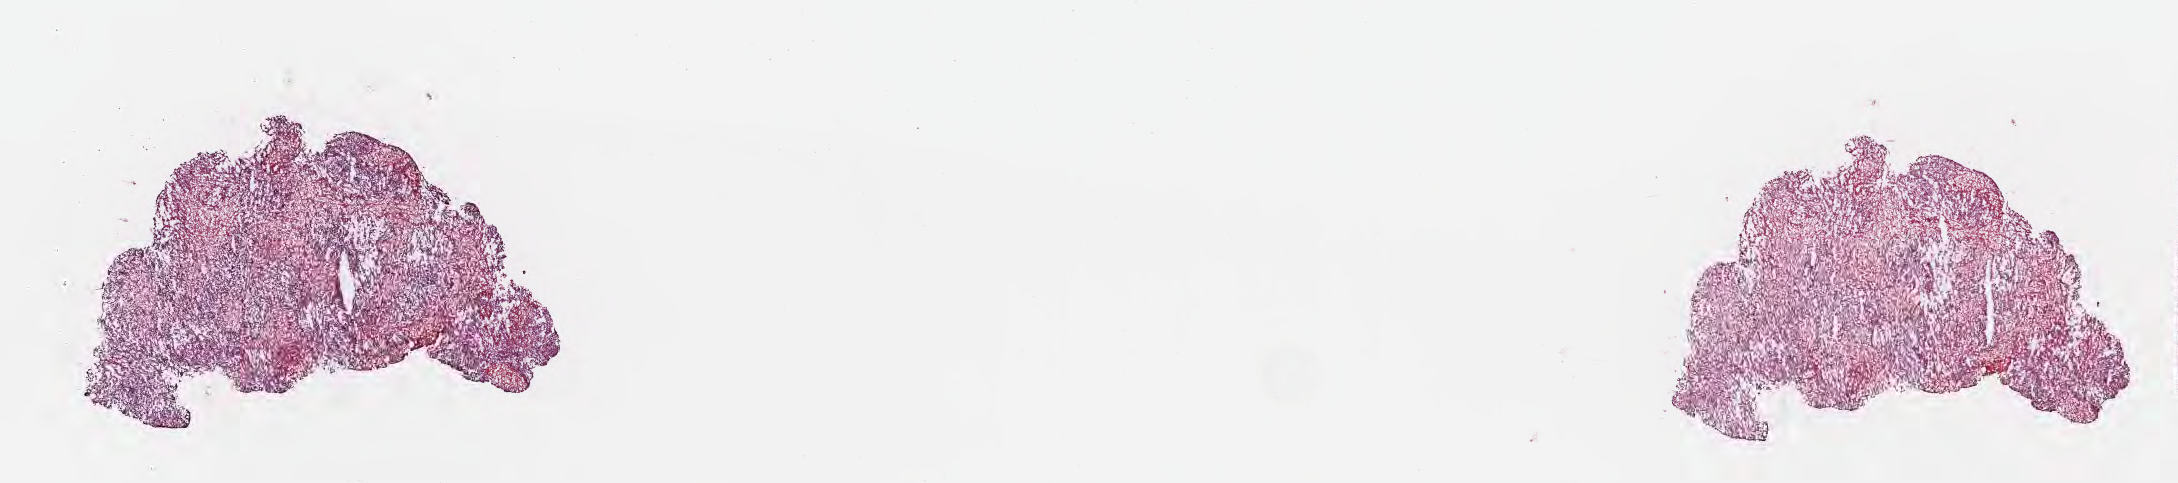
Whole-slide image, haematoxylin and eosin stain — whole scanned area (about 17.6 x 3.9 mm) shown as a low-resolution overview, frozen section (tissue freezing medium), specimen: metastatic tumor tissue, resected from brain. Patient: male, age at initial diagnosis 73 years. Pathologist review of this section (percent, as recorded): tumor cells 50%, tumor nuclei 60%, stromal cells 50%, necrosis 0%, normal cells 0%. Inflammatory infiltration, as recorded: lymphocyte infiltration 0%, monocyte infiltration 0%, neutrophil infiltration 0%.
Patient diagnosis (primary): Malignant melanoma, NOS. Section: top of the tissue portion.